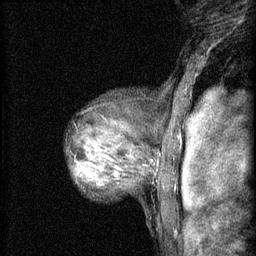
Breast MRI (dynamic contrast-enhanced), one sagittal slice; slice 48 of 60 in the series (ordered by position); 3 images stored at this slice position (order not interpretable as contrast timing); 1.5 T; TE 4.2 ms, TR 8.2 ms; 2 mm slice thickness; 256 × 256 image matrix. Female patient, age 48 years.
Structures marked on this image (semi-automatically segmented with operator editing):
- analysis volume of interest (the breast-tissue region the enhancement analysis was run in; not a lesion): box from (x=76, y=138) to (x=133, y=189) px
- tumour enhancement mask (voxels above the 70 % enhancement threshold inside the analysis volume of interest): (x=80, y=148)–(x=117, y=177)